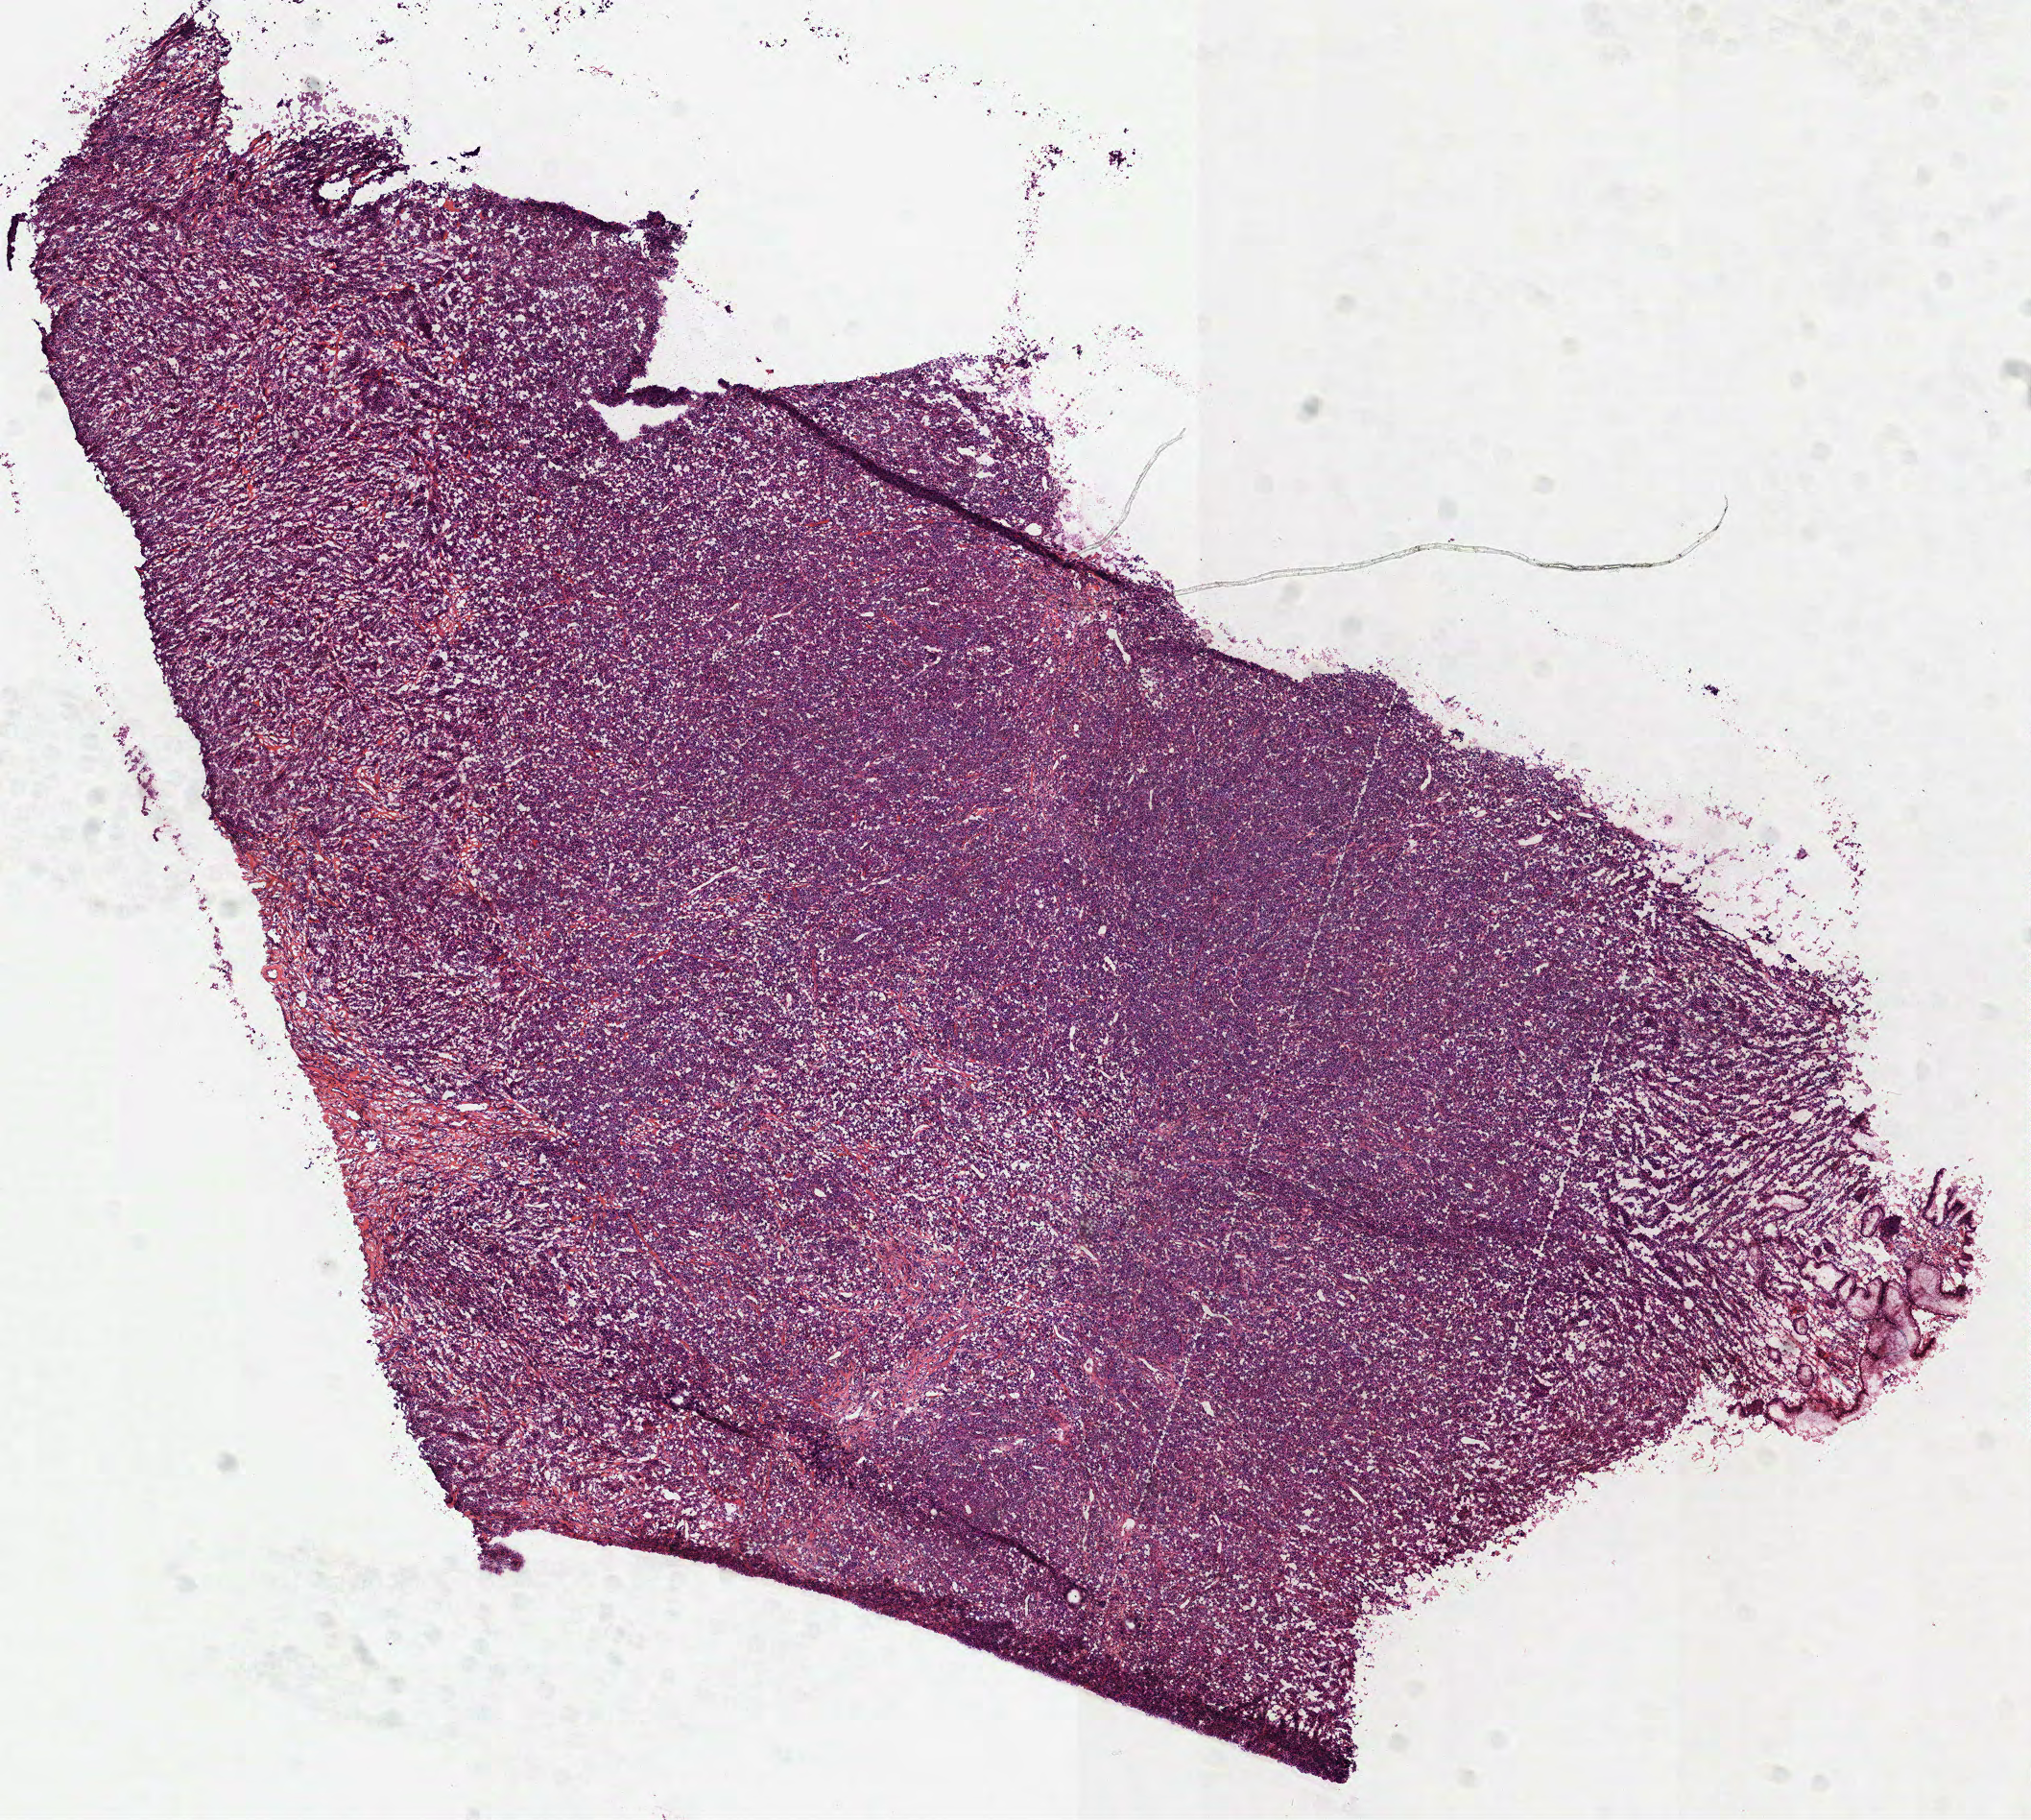
Digitized Hematoxylin and eosin (H&E) stained tissue section (whole slide), a low-resolution overview of the entire scanned area, about 8.5 x 7.6 mm (acquisition: 40x scan); frozen section from the top of the tissue portion; sample: primary tumour, stomach. Female, age 66 years at initial diagnosis. Histologic grade: G3 (poorly differentiated). Slide review estimates, as recorded: tumour cells 90%, tumour nuclei 85%, normal cells 5%, stromal cells 5%, necrosis 0%.
• histologic diagnosis: Carcinoma, diffuse type (fundus of stomach)
• AJCC pathologic stage: IIIA (6th edition)
• lymph nodes positive (case pathology): 2 of 7 examined